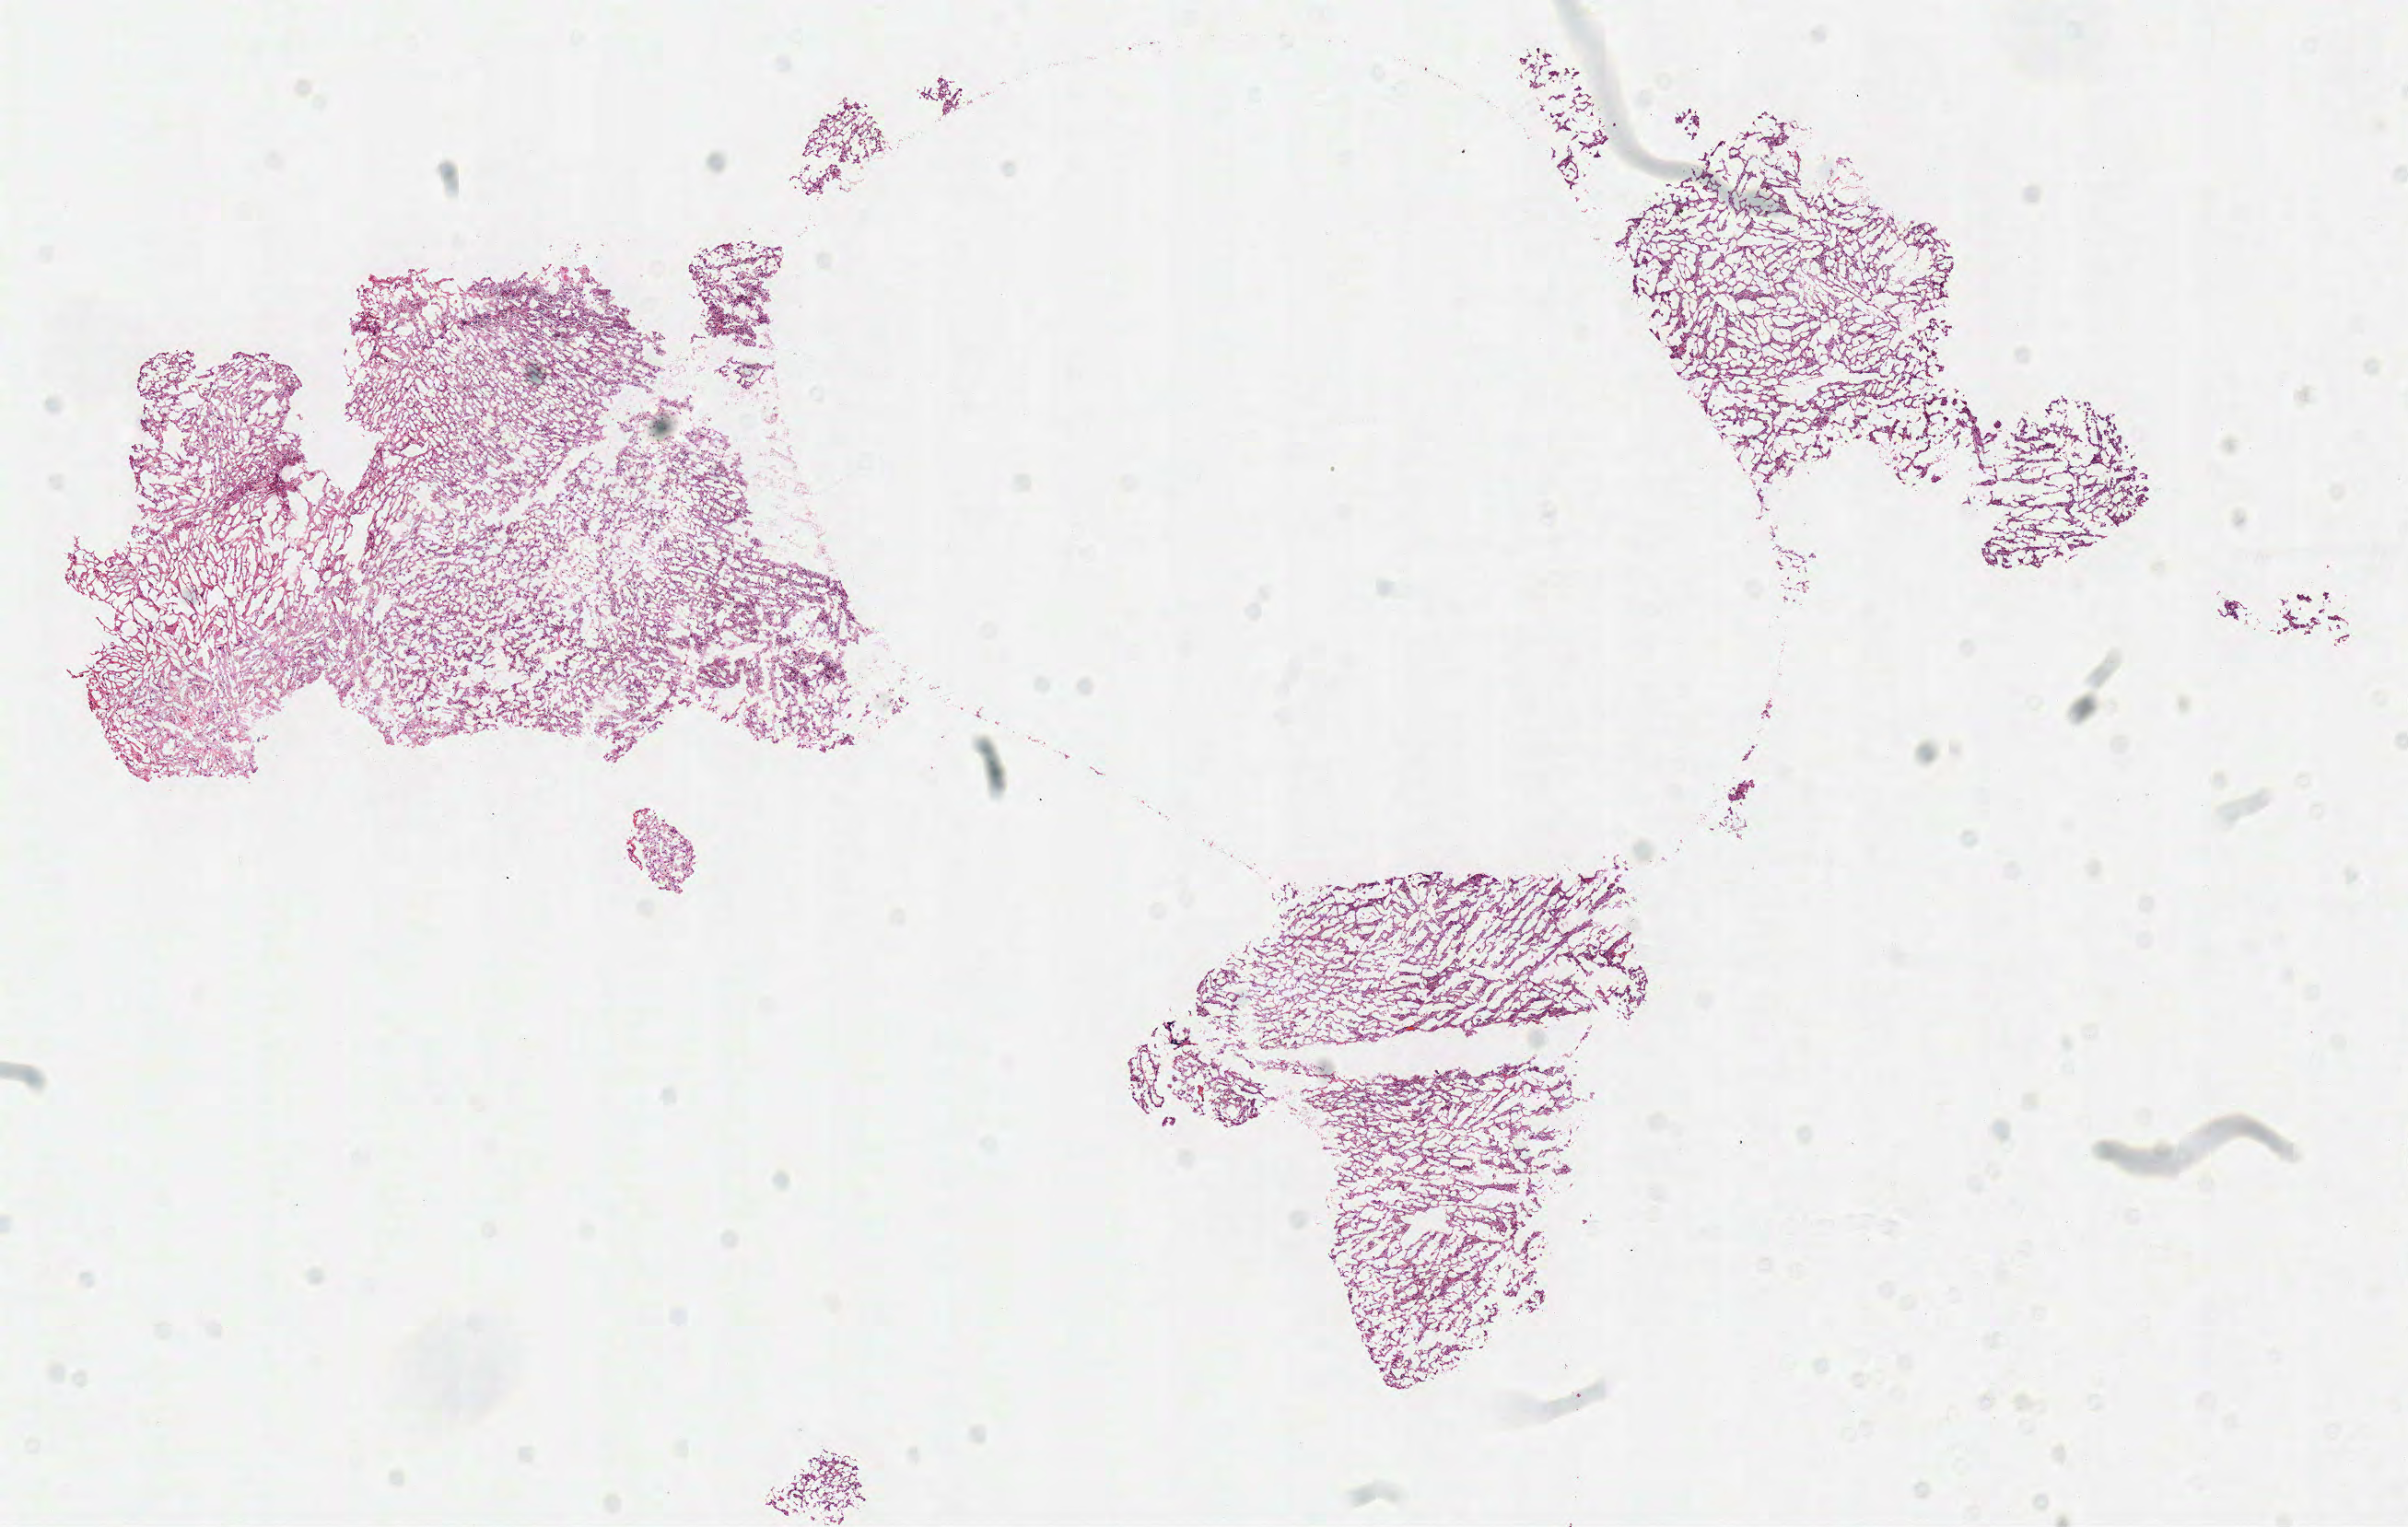
Whole-slide histology image, H&E — shown as a low-resolution overview of the whole scanned area (about 10.3 x 6.5 mm, slide scanned at 40x); frozen section; brain, primary tumour sample. Male, age 56 years at initial diagnosis. Composition of this section per pathologist review: tumour cells 100%, tumour nuclei 70%, normal cells 0%, stromal cells 0%, necrosis 0%.
* diagnosis: Glioblastoma